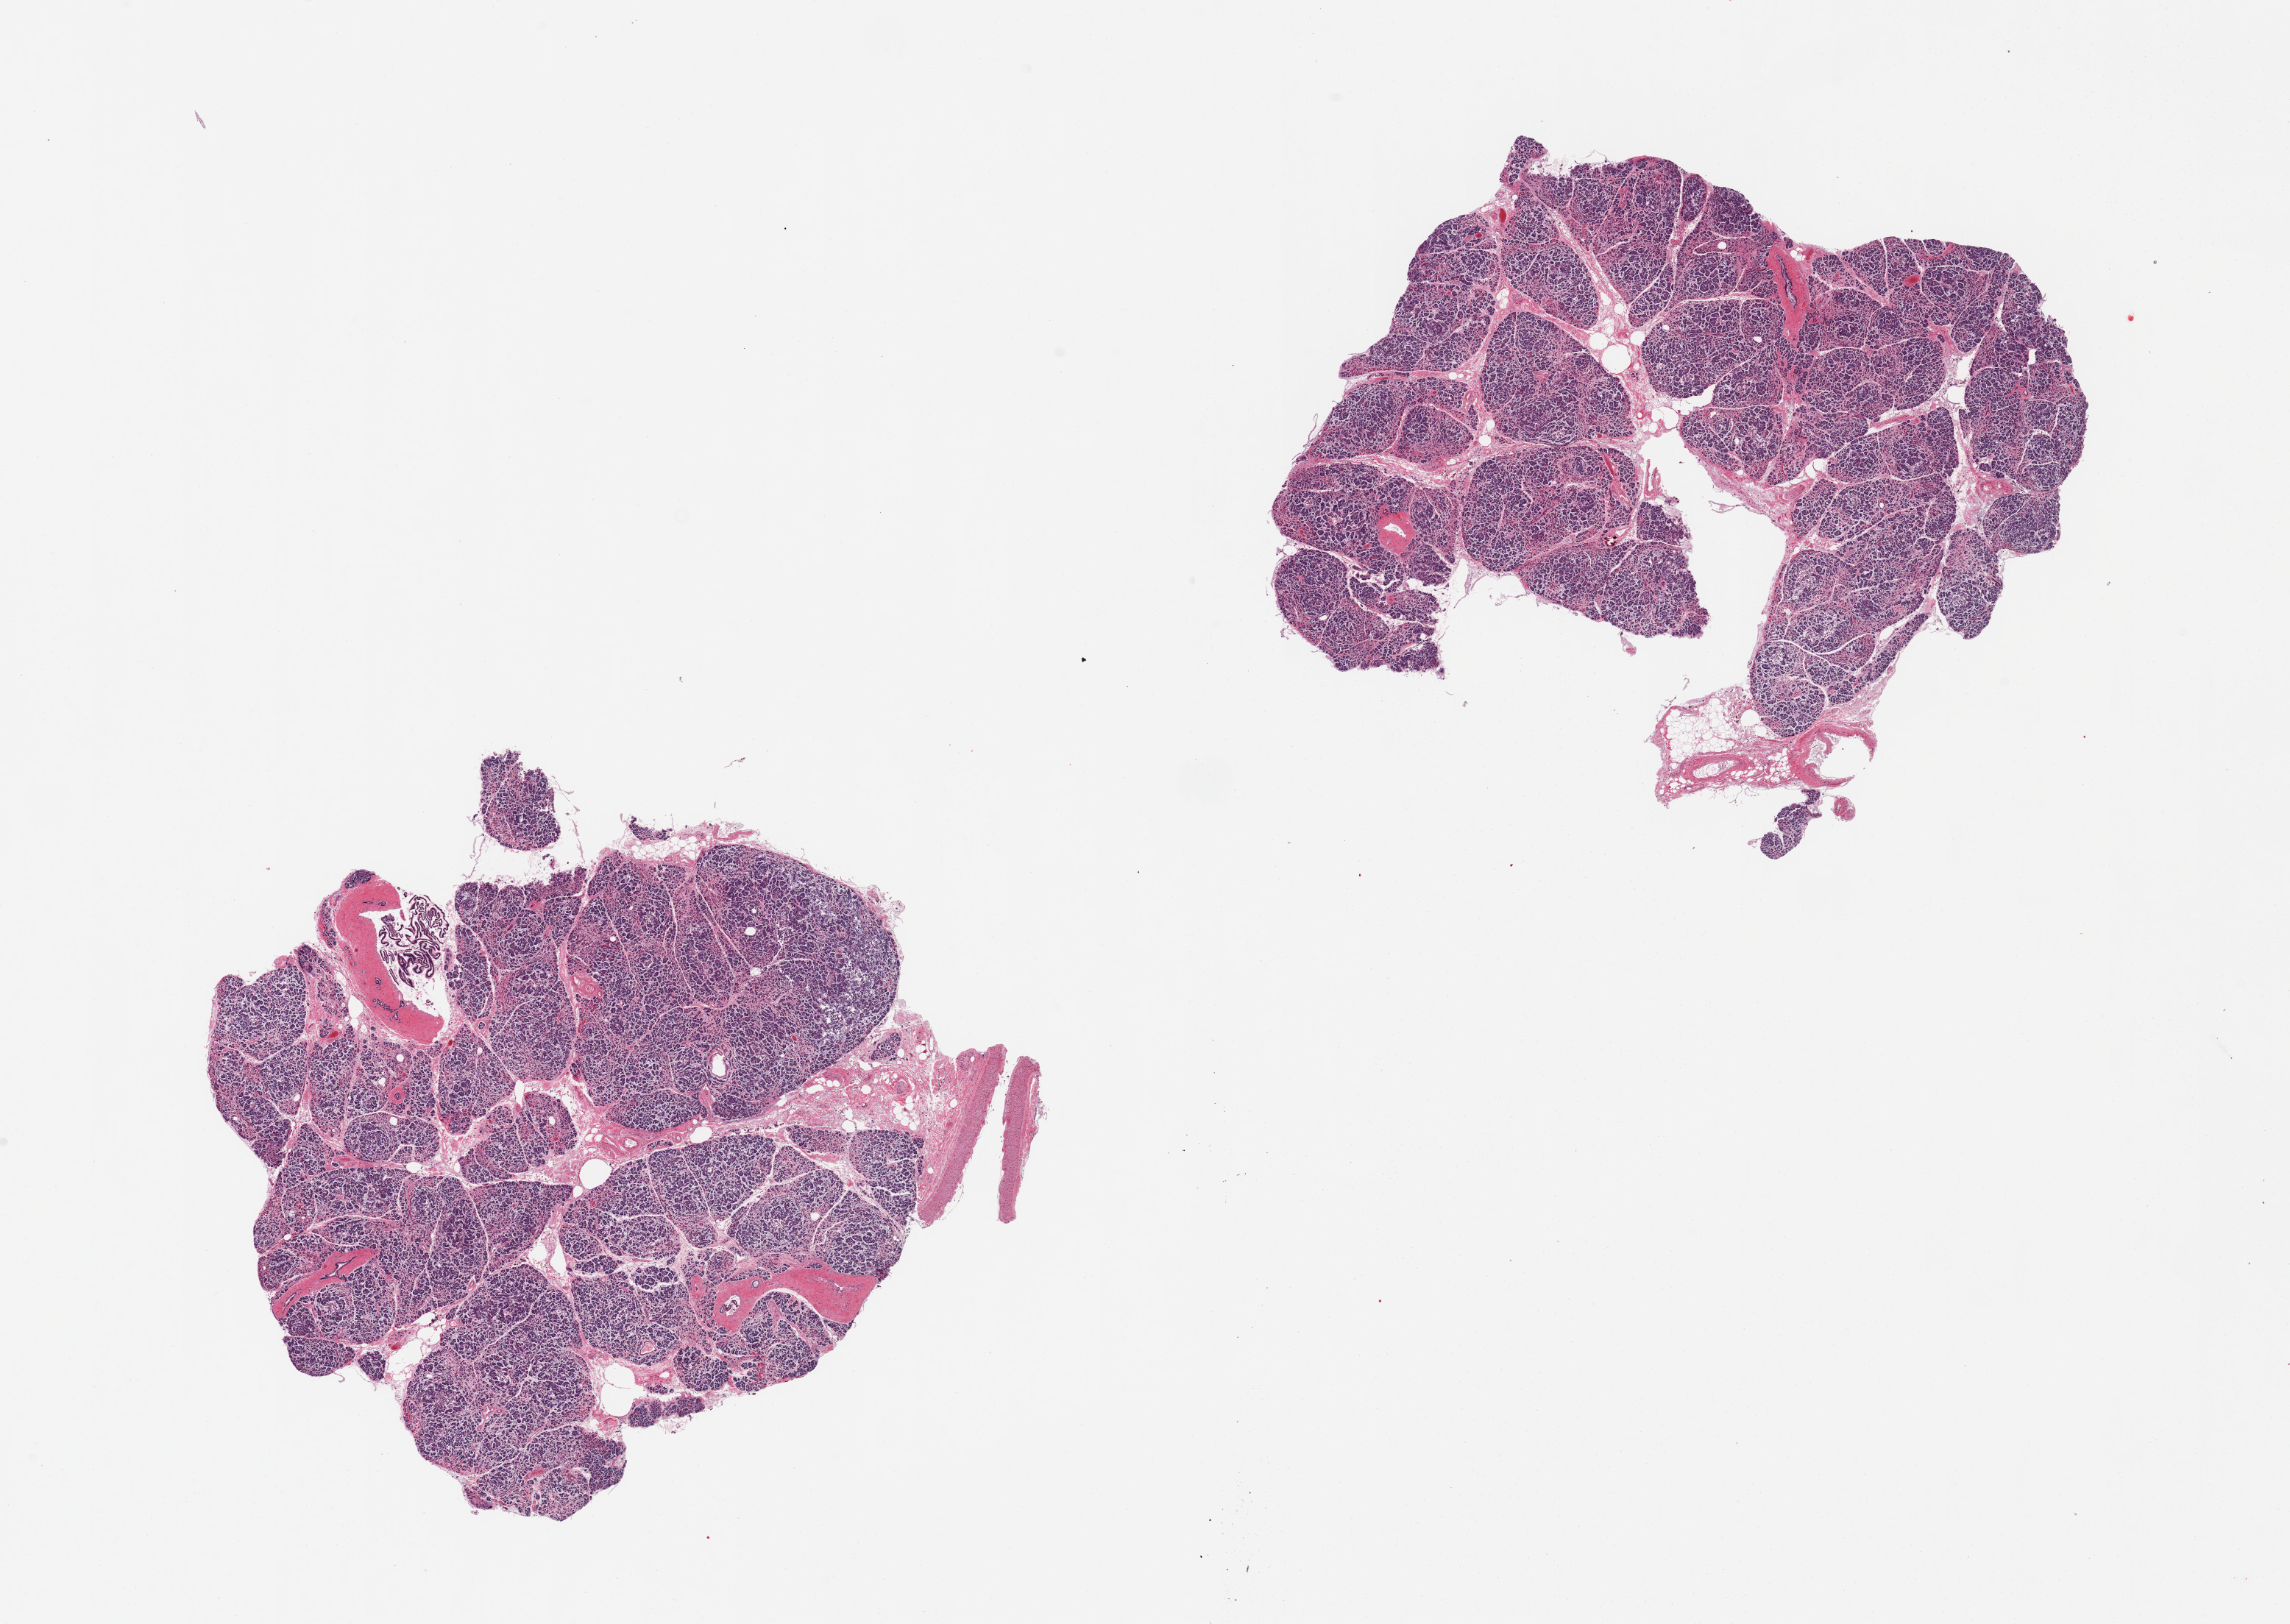
Haematoxylin and eosin whole-slide image, whole scanned area (about 24.6 x 17.5 mm) shown as a low-resolution overview. PAXgene-fixed, paraffin-embedded tissue. Sampled site (target tissue): pancreas. Donor tissue sample. Donor: male.
* pathologist's review note for this sample: 2 pieces. Well trimmed